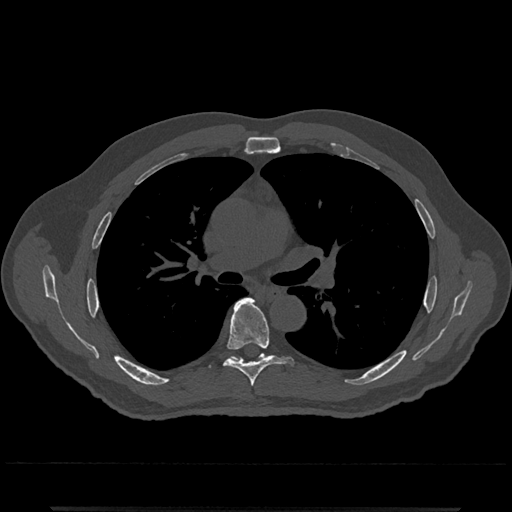
CT including the spine, one axial slice; reconstruction kernel Br40s/3; bone window (W 1800 / L 400 HU); 0.5 mm slice thickness; 512 × 512 image matrix, field of view 393 × 393 mm. Male patient, age 67 years. From the clinical record (not read from this slice): primary cancer: prostate.
Annotated regions visible in this slice (semi-automatically segmented with operator editing):
- T6 vertebra: bounding box <224,298,292,387> (left, top, right, bottom; pixels)
- T7 vertebra: <260,354,265,356>